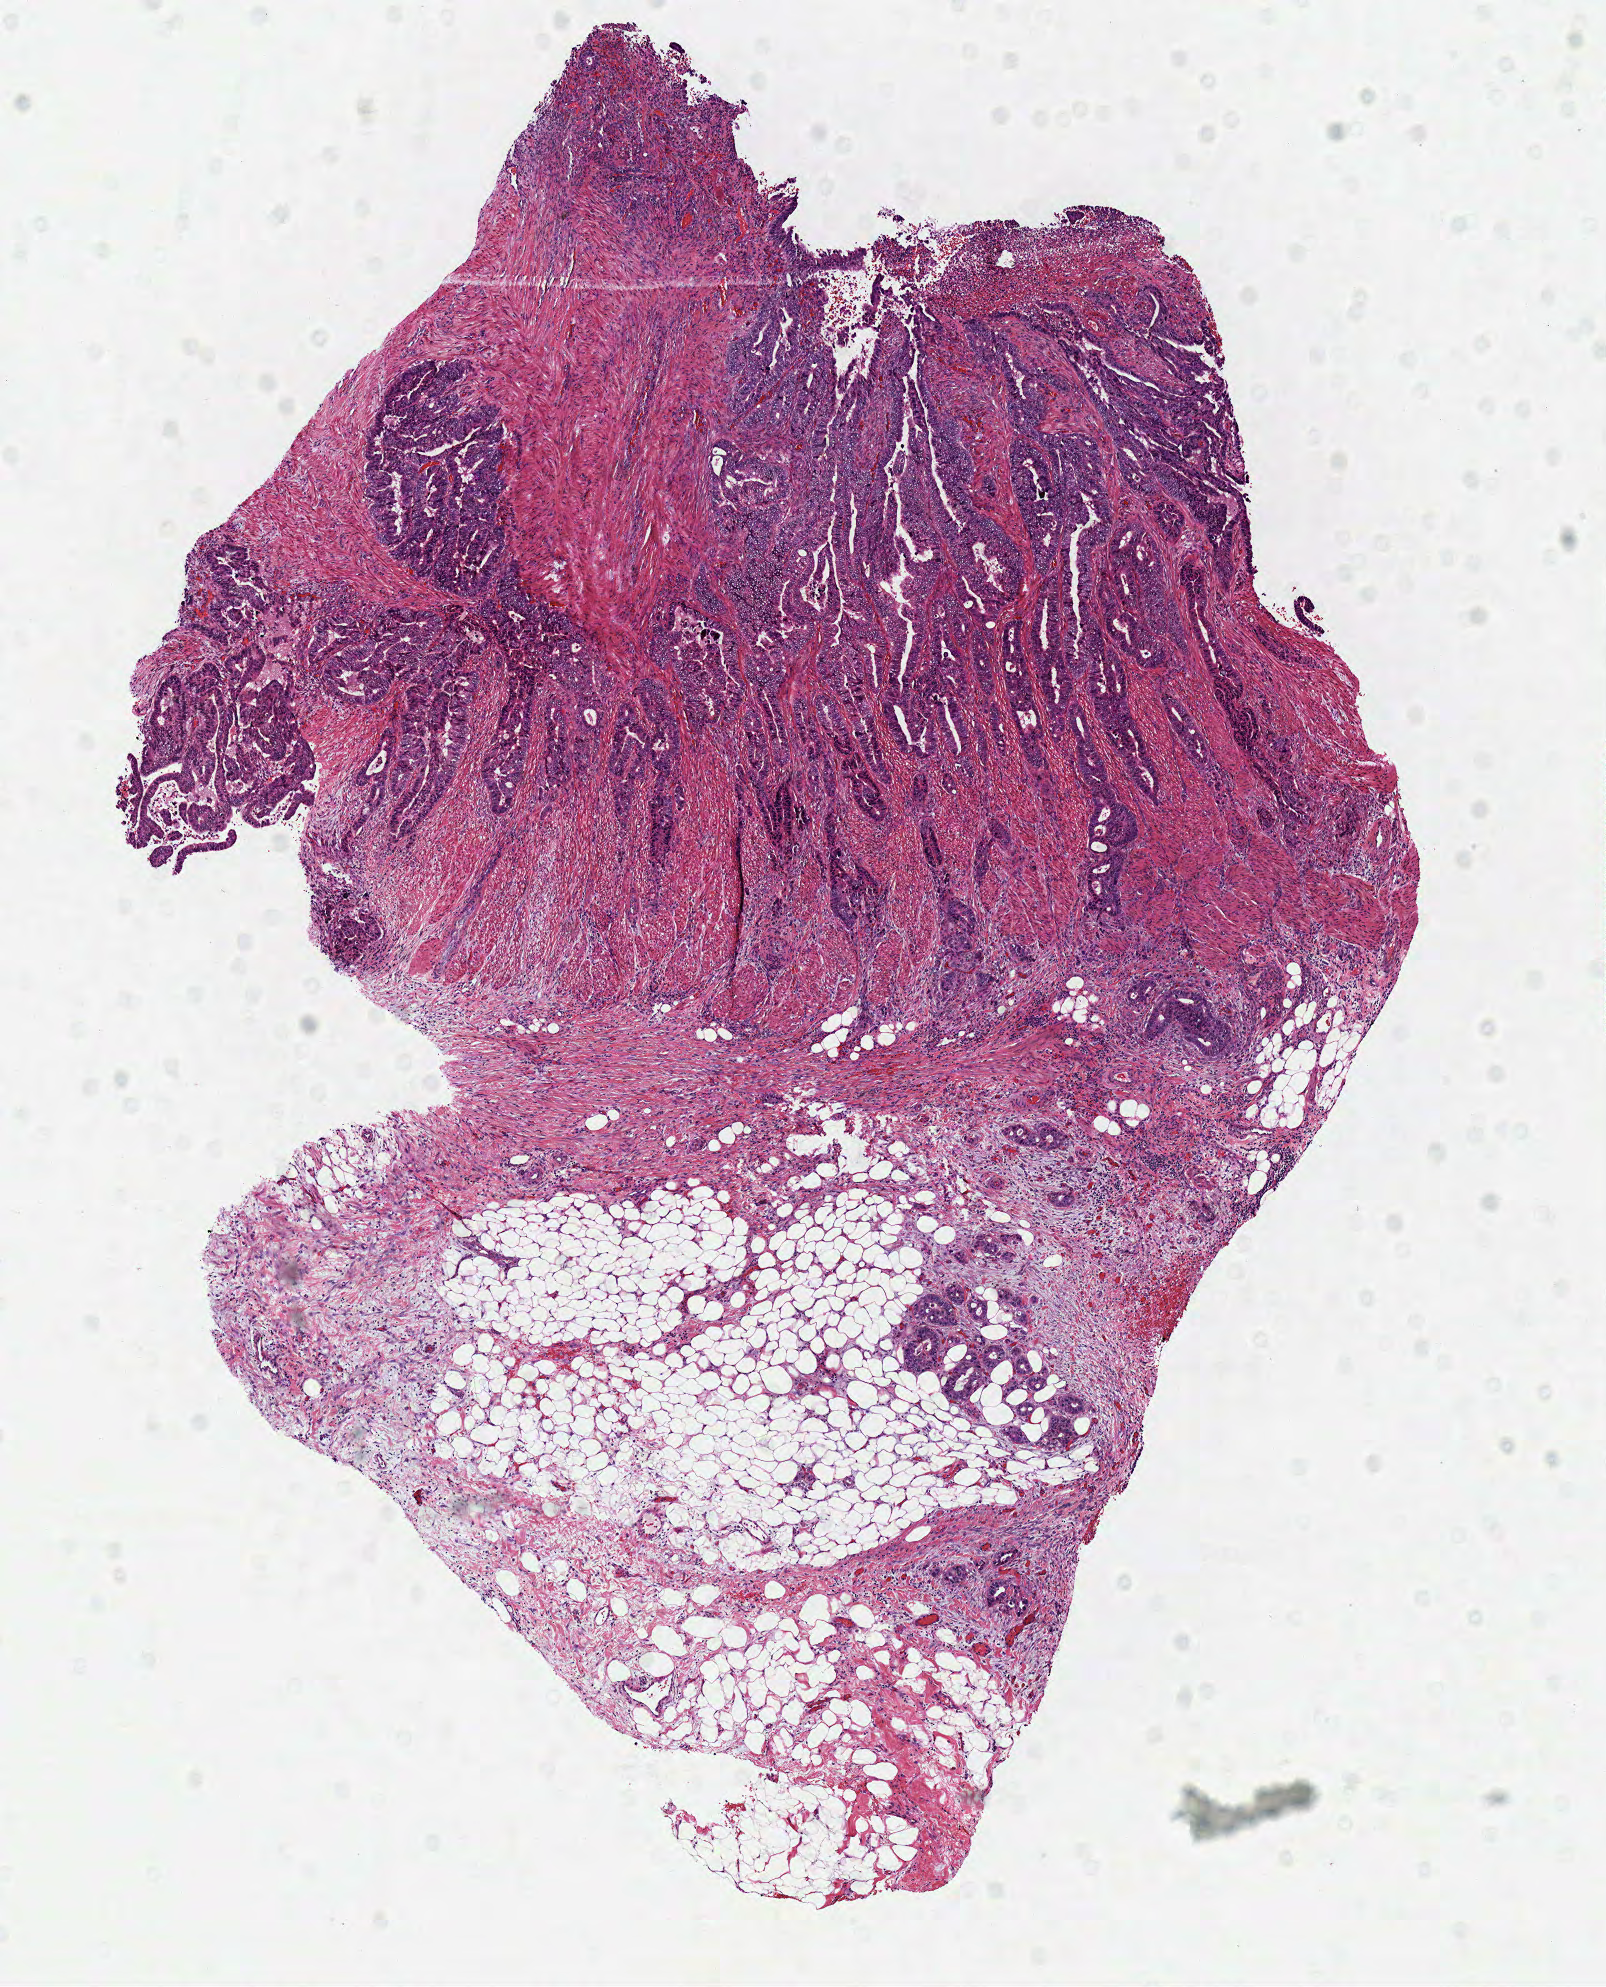
Digitized H&E-stained tissue section (whole slide), shown as a low-resolution overview of the whole scanned area (about 6.3 x 7.8 mm). Frozen section from the top of the tissue portion. Sample: primary tumour, colon. Female, age 56 years at initial diagnosis. Composition of this section per pathologist review: tumour cells 50%, tumour nuclei 75%, normal cells 0%, stromal cells 50%, necrosis 0%. Inflammatory infiltration, as recorded: lymphocyte infiltration 5%, monocyte infiltration 0%, neutrophil infiltration 2%.
AJCC pathologic stage: IVA (7th edition). Histologic diagnosis: Adenocarcinoma, NOS (sigmoid colon). TNM: T3 N1a M1a.